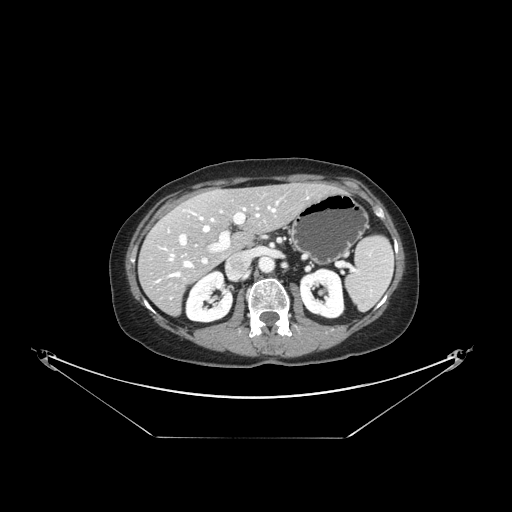
Contrast-enhanced abdominal CT, one axial slice; position 84 of 148 along the scan axis; reconstruction kernel STANDARD; 120 kVp; intravenous contrast given; soft-tissue window (W 400 / L 40 HU); 512 × 512 image matrix, field of view 500 × 500 mm. Female patient, age 73 years. From the clinical record (not read from this slice): diagnosis: colorectal cancer liver metastases, imaged before liver resection; multiple liver metastases: no; largest metastasis: 1 cm; chemotherapy before resection: yes.
Structures marked on this image (expert manual segmentation):
- hepatic veins: box from (x=164, y=205) to (x=276, y=277) px
- liver: (x=141, y=184)–(x=333, y=315)
- planned liver remnant (the part of the liver to remain after resection): (x=168, y=184)–(x=332, y=251)
- portal vein (with intrahepatic branches): (x=179, y=207)–(x=259, y=264)